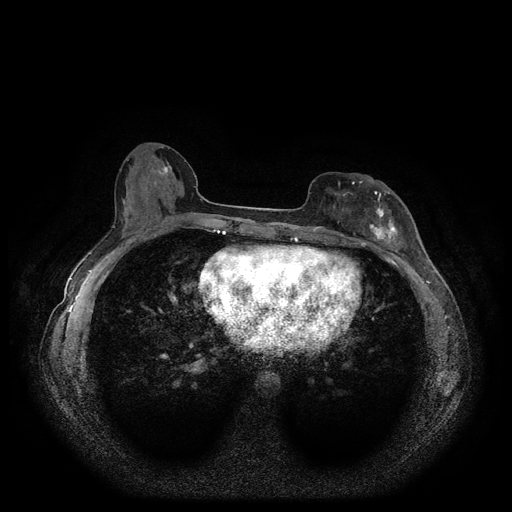
Breast MRI (dynamic contrast-enhanced, multi-phase), one axial slice. Position 46 of 116 along the scan axis. Dynamic contrast-enhanced series, time point 2 of 5 at this slice position (early post-contrast). 1.5 T. TE 2.6 ms, TR 5.3 ms. 2 mm slice thickness. 512 × 512 image matrix, field of view 350 × 350 mm. Patient: female, 51 years.
Outlined on this slice (semi-automatically segmented with operator editing):
- breast lesion (labelled 'tumour' in the annotation; benign lesions carry a separate 'benign' label): bounding box [x1, y1, x2, y2] px = [364, 200, 401, 247]
- breast lesion (labelled benign in the annotation): [156, 159, 174, 180]